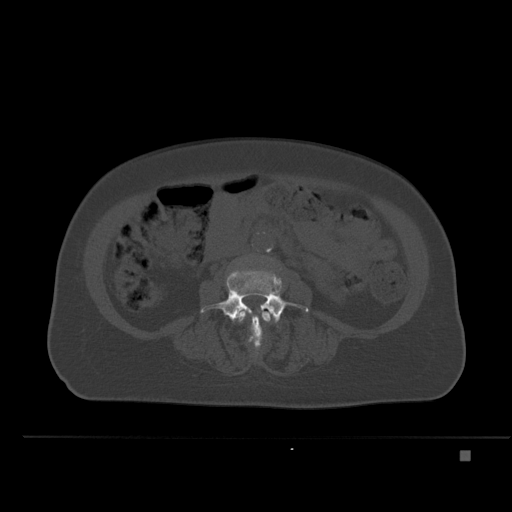
CT including the spine, one axial slice. Position 184 of 477 along the scan axis. Bone window (W 1800 / L 400 HU). 512 × 512 image matrix, field of view 422 × 422 mm. Female patient, age 74 years. Case-level facts recorded for this patient, not image findings: primary cancer: colon.
Structures marked on this image (semi-automatic segmentation, software-assisted and operator-edited):
- L3 vertebra: bounding box [x1, y1, x2, y2] px = [238, 310, 274, 347]
- L4 vertebra: [200, 271, 309, 347]